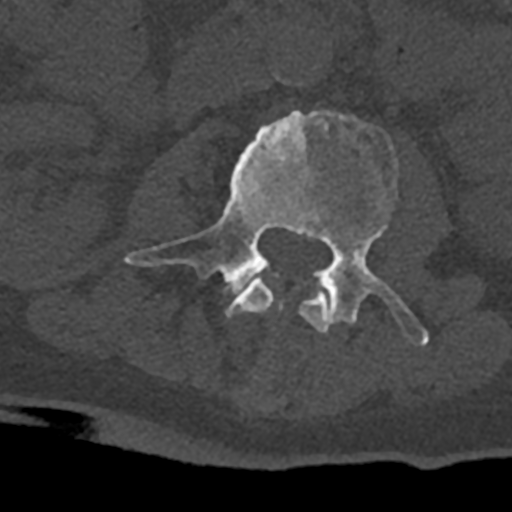
CT including the spine, one axial slice. Position 333 of 797 along the scan axis. Reconstruction kernel Br40s/3. 120 kVp. Bone window (W 1800 / L 400 HU). 512 × 512 image matrix, field of view 160 × 160 mm. Male patient, age 74 years. Case-level facts recorded for this patient, not image findings: primary cancer: renal.
Outlined on this slice (semi-automatically segmented with operator editing):
- L2 vertebra: bounding box <226,278,329,333> (left, top, right, bottom; pixels)
- L3 vertebra: <124,110,429,346>